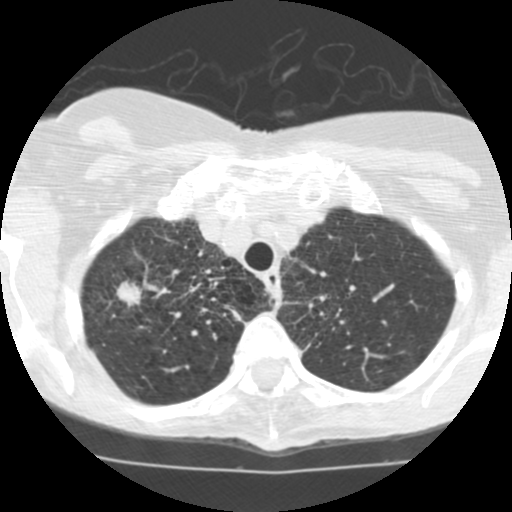
Axial slice from a low-dose chest CT screening exam. Second screening round (one year after baseline). Lung window (W 1500 / L -600 HU). 2.5 mm slice thickness. Standard (soft-tissue) reconstruction kernel (STANDARD). Slice 21 of 115 in the series. Female participant, aged 68 years at enrolment. Current smoker at enrolment.
• Lesion marked by an expert reader, bounding box <85,266,155,338> (left, top, right, bottom; pixels).
• The screening reader recorded 3 non-calcified nodules or masses ≥4 mm on this exam (right upper lobe, right upper lobe, right middle lobe); which of them this box marks is not recorded.
• Official screen result: positive, other.
• Later outcome: lung cancer diagnosed 36 days after this screen — large cell neuroendocrine carcinoma, right upper lobe, undifferentiated (G4), stage IB (AJCC 6th edition), 22 mm at pathology.